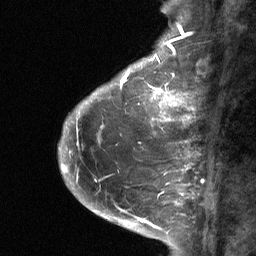
Breast MRI (dynamic contrast-enhanced), one sagittal slice; slice 20 of 64 in the series (ordered by position); dynamic contrast-enhanced study with each time point stored as its own series, time point 2 of 3 at this slice position (early post-contrast, ordered by acquisition time); 1.5 T; TE 4.8 ms, TR 27 ms; 2 mm slice thickness; 256 × 256 image matrix, field of view 180 × 180 mm. Patient: female, 59 years. Case-level facts recorded for this patient, not image findings: setting: breast cancer imaged before/during neoadjuvant chemotherapy; receptor status: triple-negative.
Outlined on this slice (semi-automatic segmentation, software-assisted and operator-edited):
- analysis volume of interest (the breast-tissue region the enhancement analysis was run in; not a lesion): box from (x=113, y=85) to (x=175, y=120) px
- tumour enhancement mask (voxels above the 90 % enhancement threshold inside the analysis volume of interest): (x=150, y=90)–(x=164, y=102)